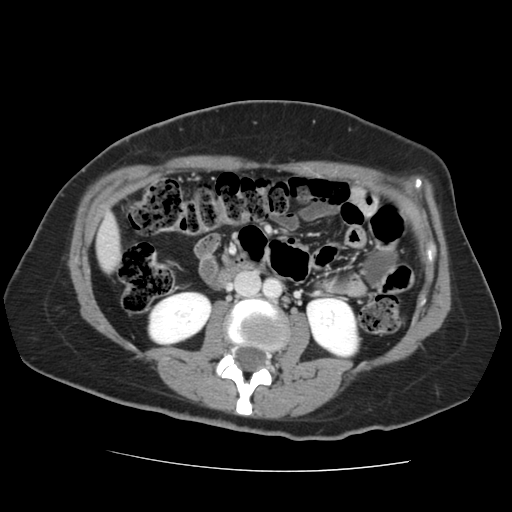
Contrast-enhanced abdominal CT, one axial slice; slice 42 of 144 in the series (ordered by position); 120 kVp; soft-tissue window (W 400 / L 40 HU); 2.5 mm slice thickness; 512 × 512 image matrix, field of view 333 × 333 mm. Female patient, age 46 years. Case-level facts recorded for this patient, not image findings: diagnosis: colorectal cancer liver metastases, imaged before liver resection; multiple liver metastases: no; largest metastasis: 2.8 cm; chemotherapy before resection: yes.
Structures marked on this image (expert manual segmentation):
- liver: bounding box <98,220,120,270> (left, top, right, bottom; pixels)
- planned liver remnant (the part of the liver to remain after resection): <98,222,120,269>